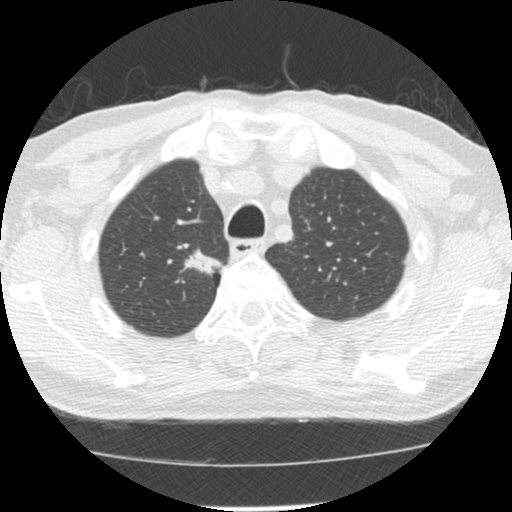
Chest CT (low-dose screening protocol), one axial image; baseline screening round; lung window (W 1500 / L -600 HU); standard (soft-tissue) reconstruction kernel (STANDARD); 120 kVp; slice 30 of 139 in the series; 512 × 512 image matrix. Male participant, aged 64 years at enrolment. Former smoker at enrolment.
• Expert-annotated lung lesion, bounding box [x1, y1, x2, y2] px = [175, 236, 224, 278].
• The exam's reader record, not a measurement of the box and not confirmed to be the same lesion: non-calcified nodule or mass ≥4 mm, right upper lobe, 20 × 13 mm, spiculated (stellate) margins, soft tissue attenuation.
• Later outcome: lung cancer diagnosed 73 days after this screen — adenocarcinoma, NOS, right upper lobe, moderately differentiated (G2), stage IA (AJCC 6th edition), 17 mm at pathology.